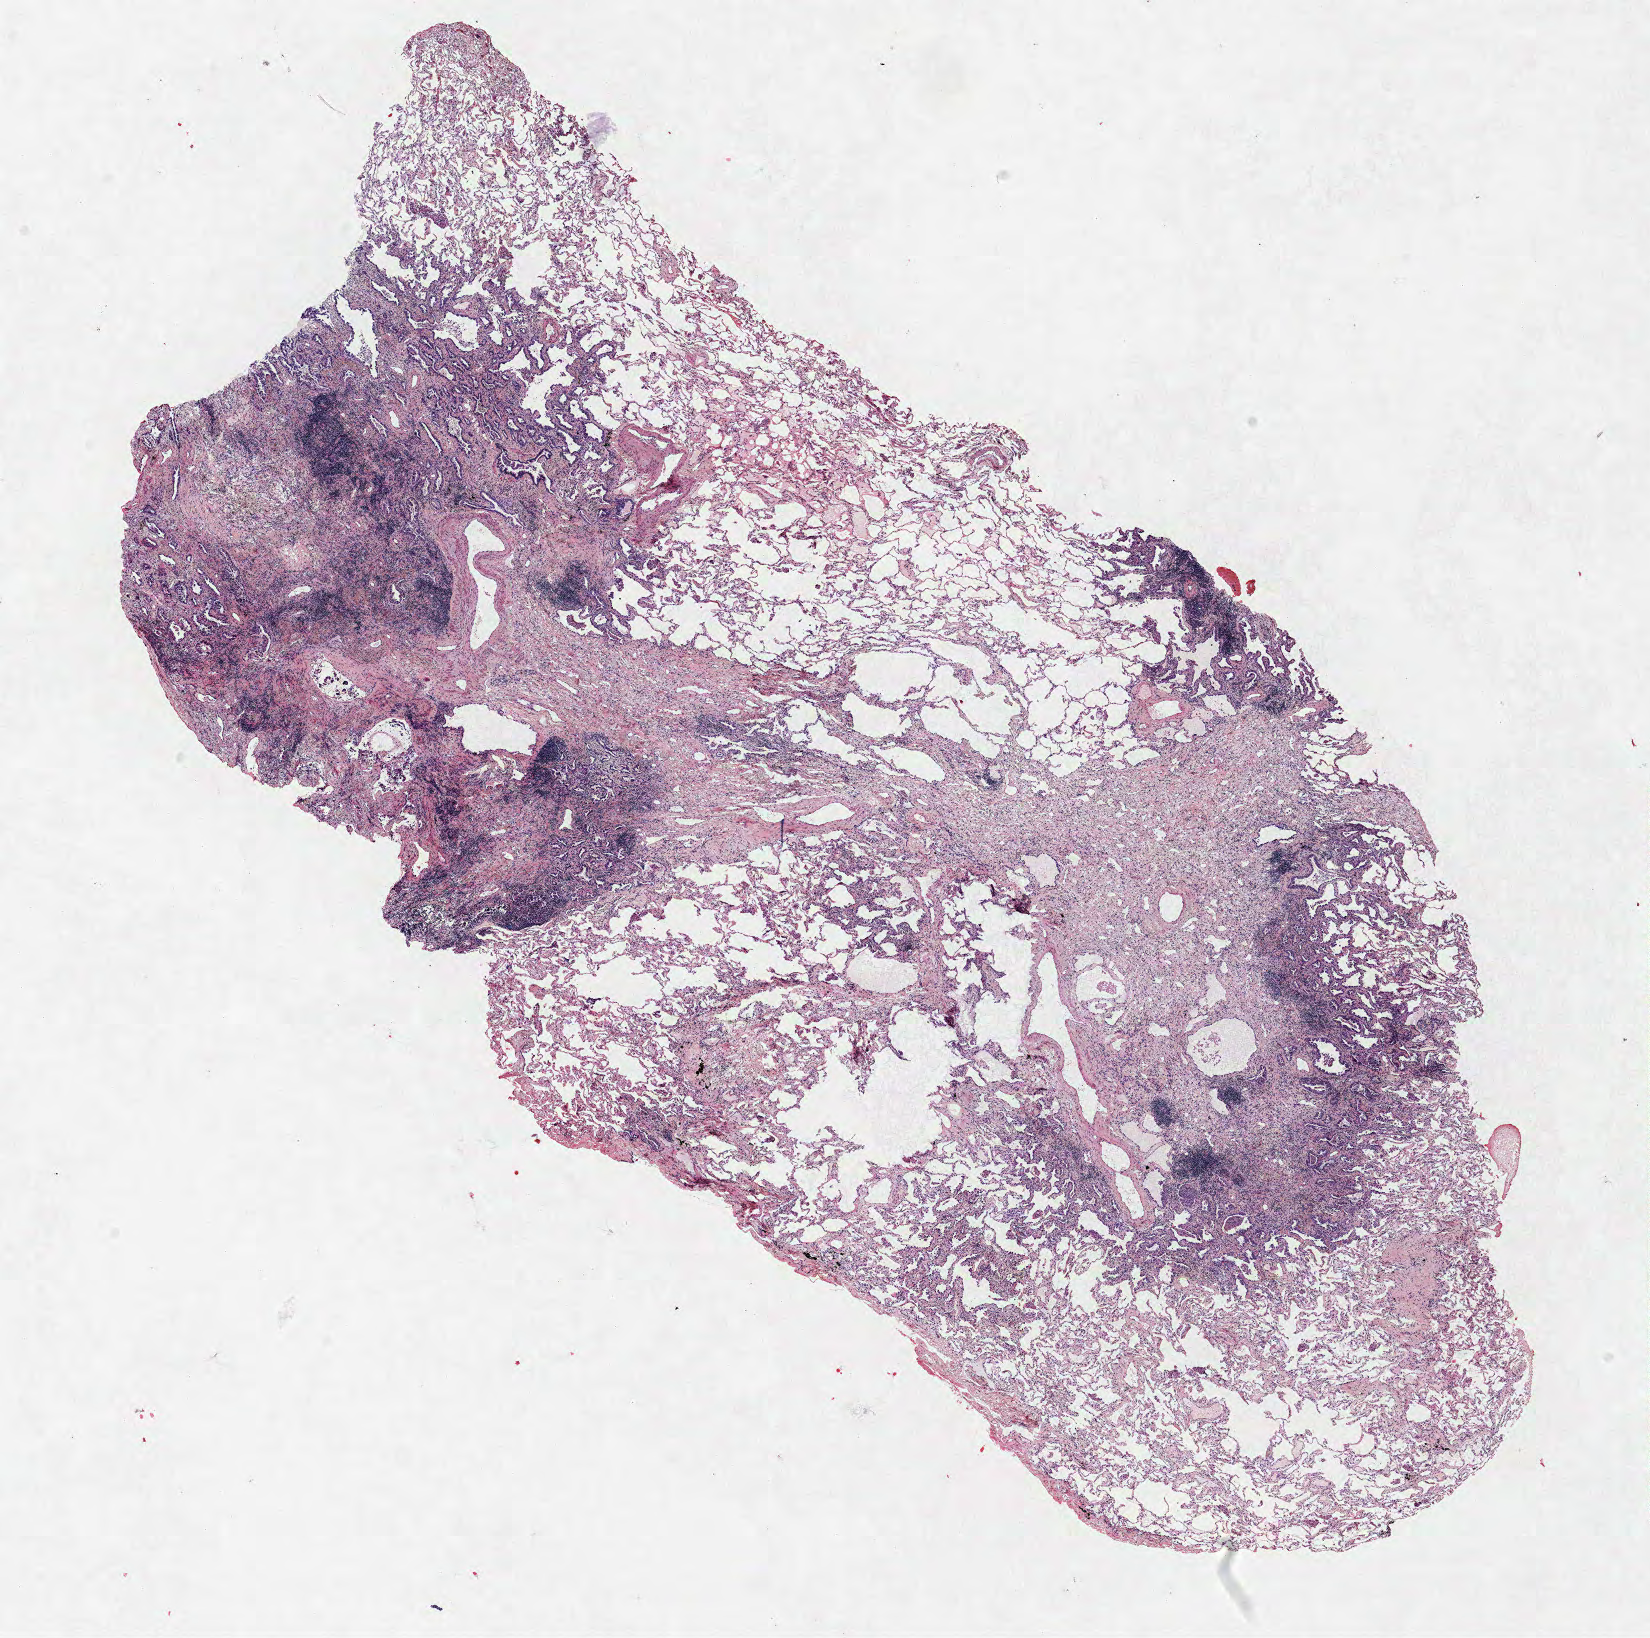
Whole-slide histology image, H&E-stained — a low-resolution overview of the entire scanned area, about 13.2 x 13.1 mm (from a 40x scan). Formalin-fixed paraffin-embedded (FFPE) section. Lung tissue. Female patient, aged 60 at enrolment. Former smoker at enrolment. Grade: moderately differentiated (G2).
Participant's lung-cancer diagnosis: Bronchiolo-alveolar adenocarcinoma, NOS. Stage (AJCC 6th edition): IA. Tumour size (pathology): 15 mm. Primary tumour location (clinical record): left upper lobe. Note: participant had 2 primary lung cancers recorded; fields above describe the first.